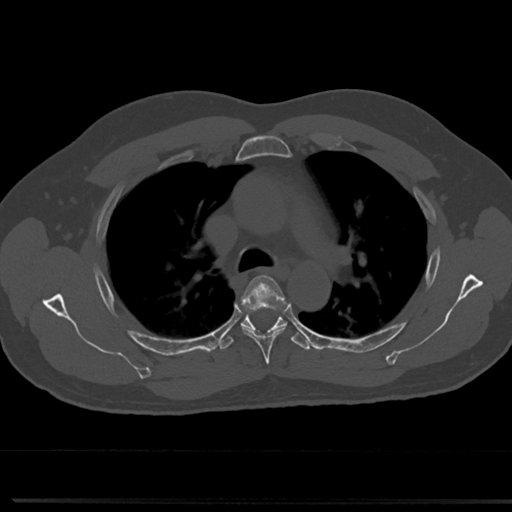
CT including the spine, one axial slice. Position 526 of 817 along the scan axis. 120 kVp. Bone window (W 1800 / L 400 HU). 512 × 512 image matrix, field of view 355 × 355 mm. Male patient, age 61 years. From the clinical record (not read from this slice): primary cancer: prostate.
Outlined on this slice (semi-automatically segmented with operator editing):
- T4 vertebra: bounding box (x1, y1, x2, y2) in pixels: (238, 275, 289, 358)
- T5 vertebra: (241, 320, 307, 345)